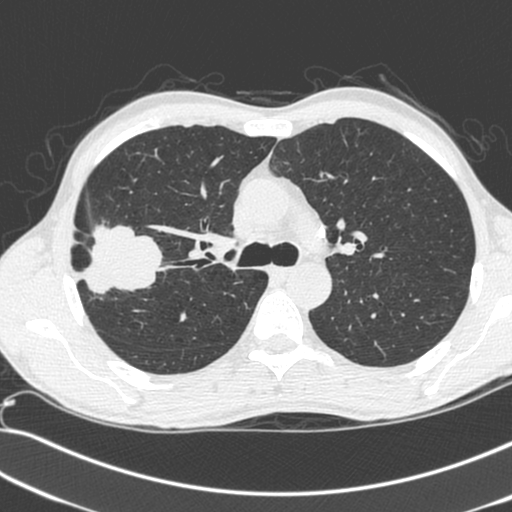
Low-dose screening chest CT, axial slice, baseline screening round, lung window (W 1500 / L -600 HU), 120 kVp, 512 × 512 image matrix. Male, age 55 years at enrolment.
• Expert reader's lesion annotation, box from (x=69, y=227) to (x=154, y=302) px.
• Screening reader's record for this exam (one nodule recorded; not confirmed to be the boxed lesion): non-calcified nodule or mass ≥4 mm, right upper lobe, 52 × 39 mm, spiculated (stellate) margins, soft tissue attenuation.
• Official screen result: positive, change unspecified: nodule(s) >= 4 mm or enlarging nodule(s), mass(es), or other non-specific abnormalities suspicious for lung cancer.